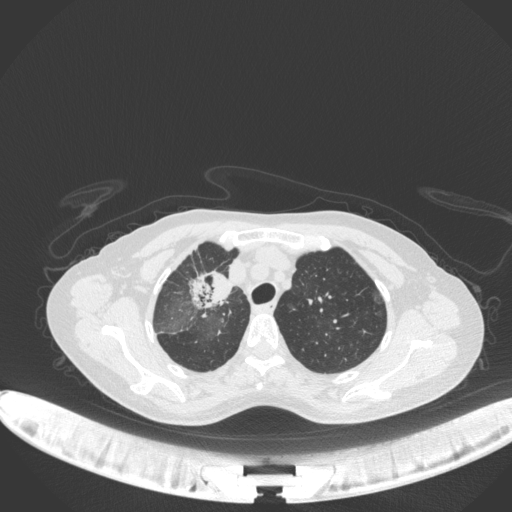
Chest CT, one axial slice. Position 256 of 311 along the scan axis. Reconstruction kernel B31f. Lung window (W 1500 / L -600 HU). 1 mm slice thickness. 512 × 512 image matrix, field of view 400 × 400 mm. Female patient, age 59 years. From the clinical record (not read from this slice): clinical TNM (as recorded): T3 N0 M0; histopathological grade: G1.
Outlined on this slice (rectangle marked by the reading radiologist):
- lung tumour (recorded histology: adenocarcinoma): bounding box (x1, y1, x2, y2) in pixels: (187, 268, 233, 318)